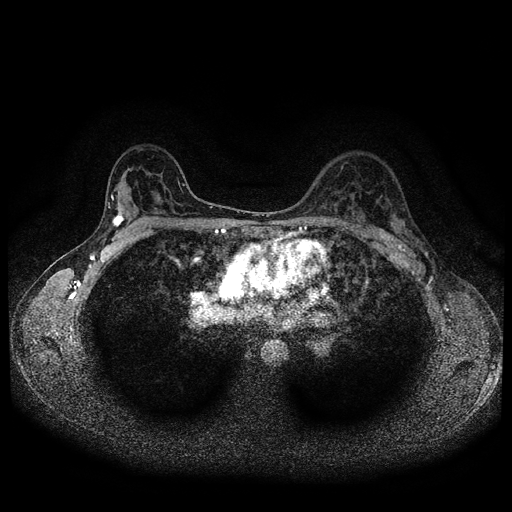
Breast MRI (dynamic contrast-enhanced, multi-phase), one axial slice; position 66 of 116 along the scan axis; dynamic contrast-enhanced series, time point 2 of 5 at this slice position (early post-contrast); 1.5 T; TE 2.7 ms, TR 5.4 ms; 512 × 512 image matrix. Patient: female, 36 years.
Structures marked on this image (semi-automatic segmentation, software-assisted and operator-edited):
- breast lesion (labelled 'tumour' in the annotation; benign lesions carry a separate 'benign' label): bounding box [x1, y1, x2, y2] px = [111, 211, 125, 229]